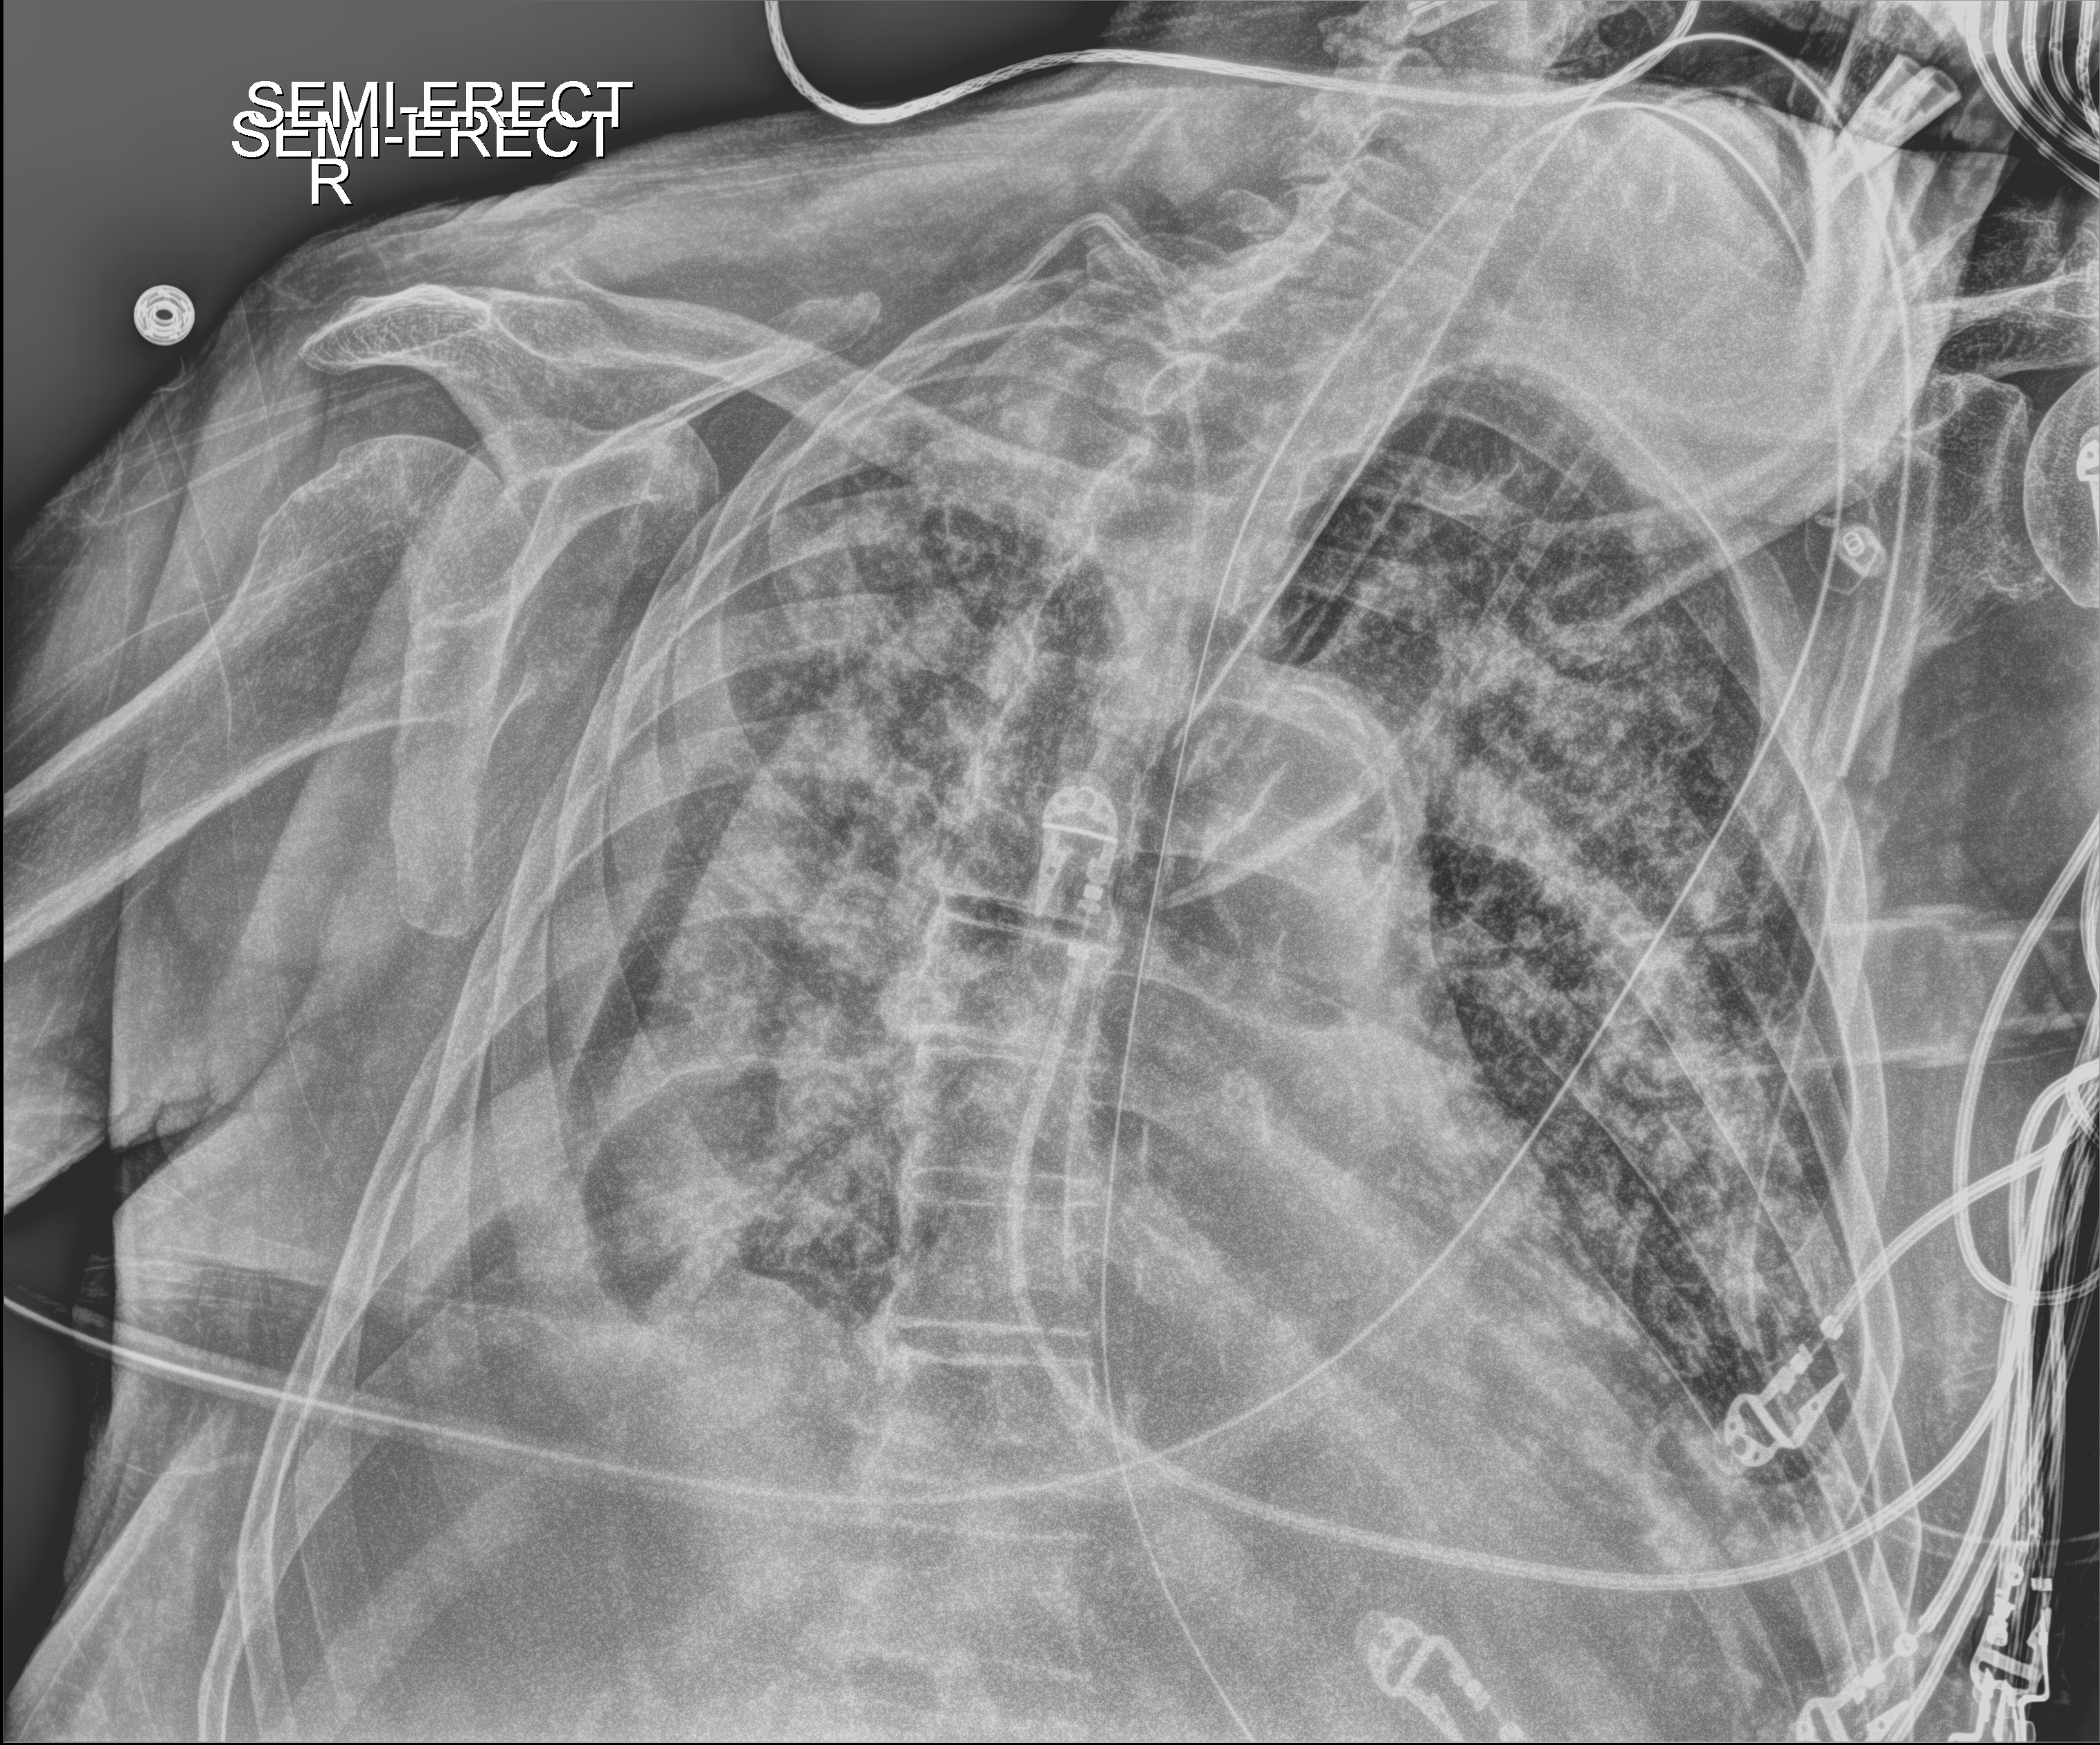
Bedside chest radiograph (digital radiography); anteroposterior (AP) projection. Male patient hospitalised with COVID-19, age 75–90 years.
Admission-level facts for this patient (not findings on this image; timing relative to this image not recorded):
- admitted to intensive care during this hospital stay: yes